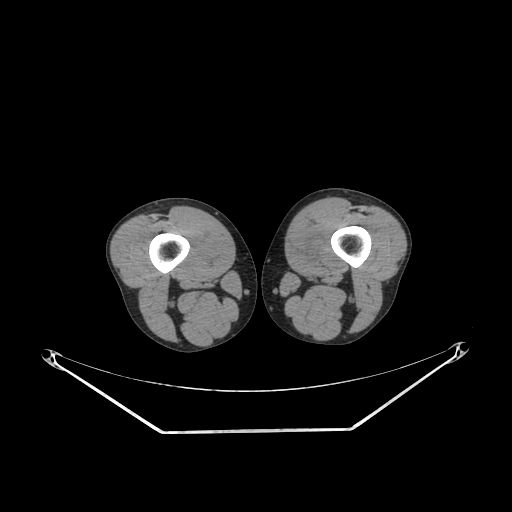
CT of an extremity soft-tissue mass (from a PET/CT study), one axial slice; slice 227 of 311 in the series (ordered by position); 140 kVp; soft-tissue window (W 400 / L 40 HU); 512 × 512 image matrix, field of view 500 × 500 mm. Male patient. From the clinical record (not read from this slice): histological type: mixoid liposarcoma; grade: low; site of the primary tumour: left thigh.
Structures marked on this image (expert contour drawn on MRI and transferred to this co-registered scan by the dataset authors):
- gross tumour volume (mass): bounding box (x1, y1, x2, y2) in pixels: (299, 238, 316, 254)